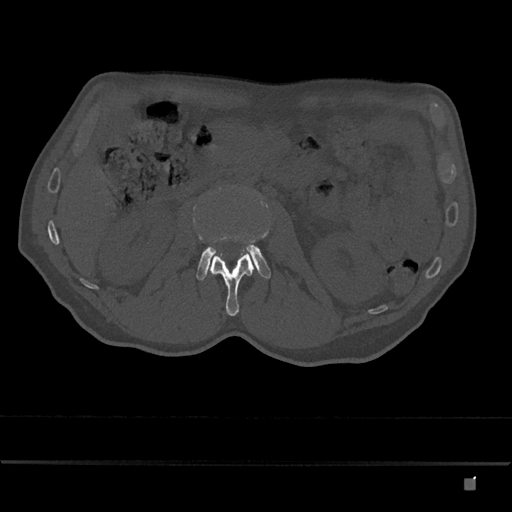
CT including the spine, one axial slice. Reconstruction kernel Br40s/3. Bone window (W 1800 / L 400 HU). 0.5 mm slice thickness. 512 × 512 image matrix, field of view 390 × 390 mm. Patient: male, 72 years. Case-level facts recorded for this patient, not image findings: primary cancer: prostate.
Structures marked on this image (semi-automatically segmented with operator editing):
- L2 vertebra: bounding box (x1, y1, x2, y2) in pixels: (207, 235, 254, 316)
- L3 vertebra: (193, 207, 271, 280)